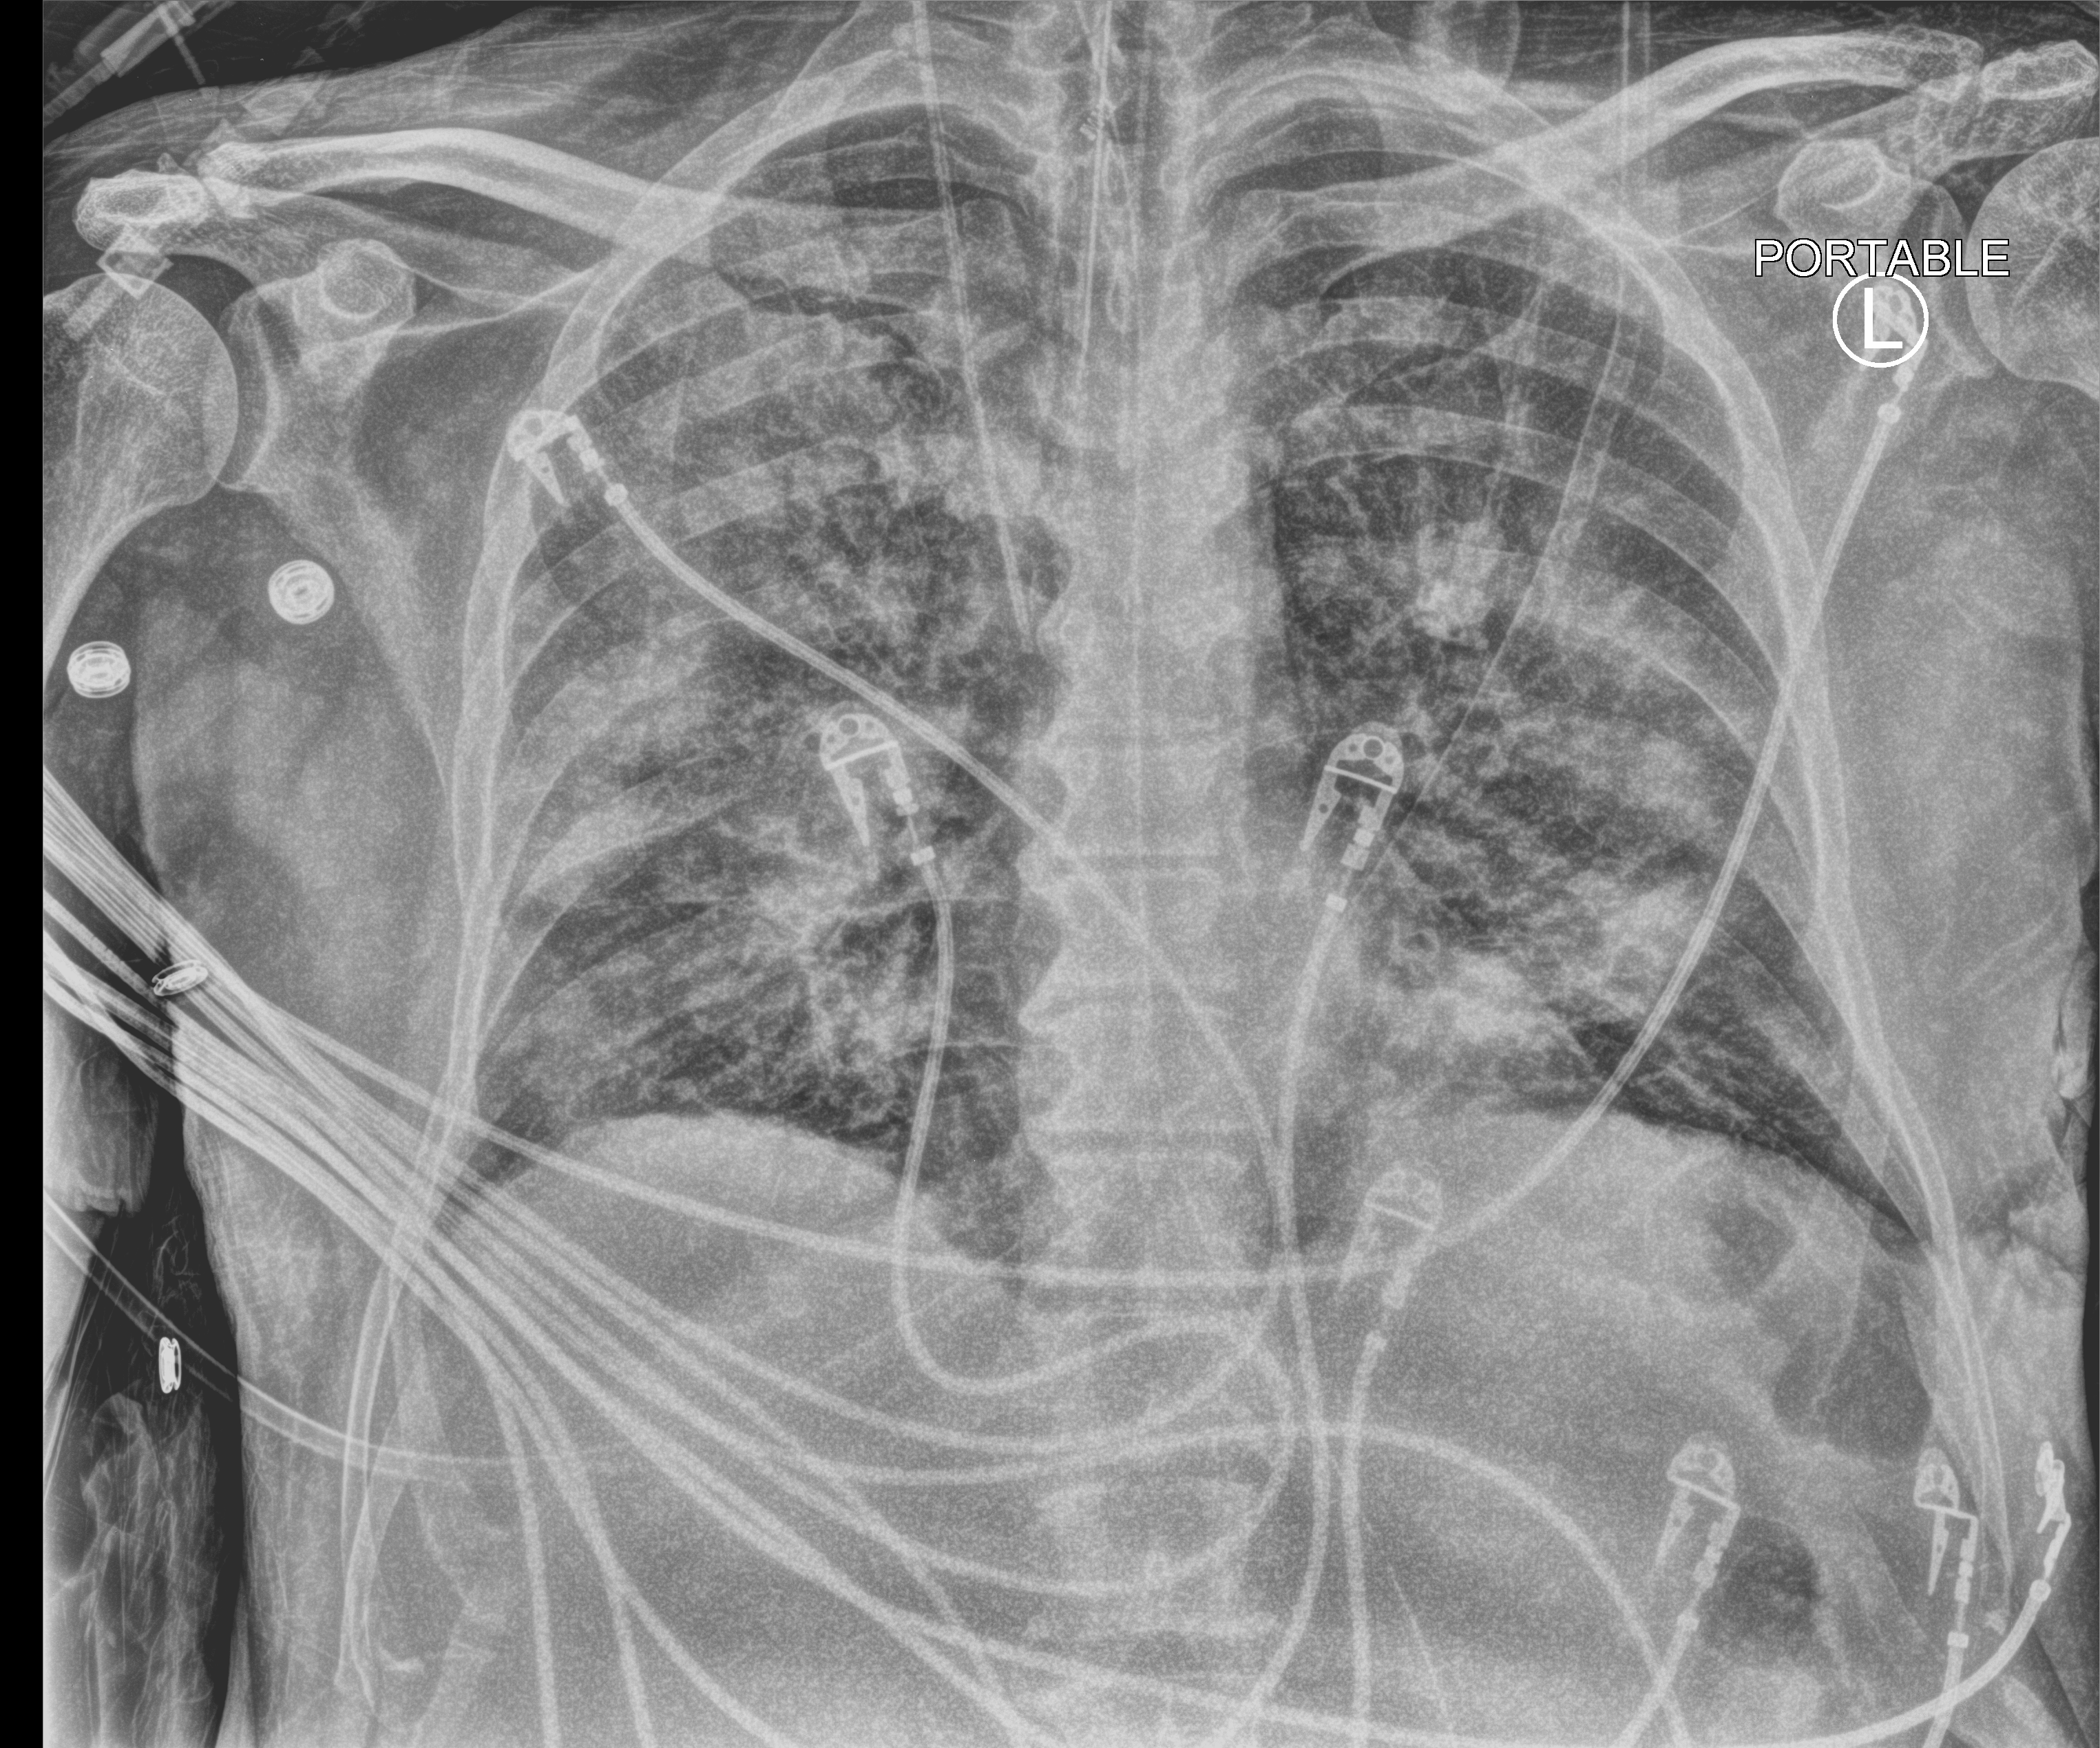
Portable chest radiograph, anteroposterior (AP) projection. Patient hospitalised with COVID-19; male, aged 60–74 years.
Hospital-stay facts (about this admission, not read from this image; timing relative to this image not recorded):
- length of hospital stay: 15 days
- admitted to intensive care during this hospital stay: yes